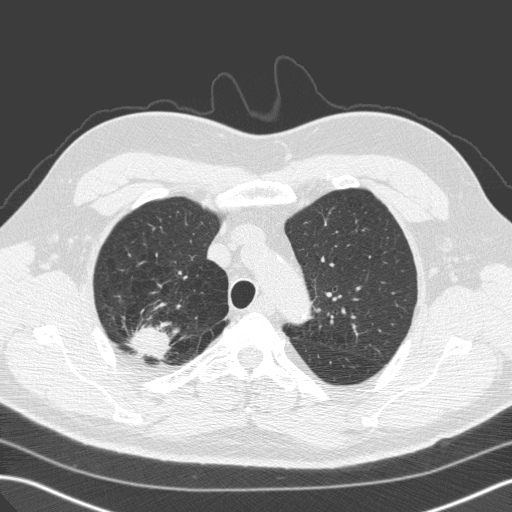
Axial slice from a low-dose chest CT screening exam. Baseline annual screen. Lung window (W 1500 / L -600 HU). 2 mm slice thickness. Standard (soft-tissue) reconstruction kernel (C). Slice 28 of 149 in the series. Male, age 59 years at enrolment.
Expert reader's lesion annotation, bounding box [x1, y1, x2, y2] px = [118, 312, 180, 367]. Screening reader's record for this exam (one nodule recorded; not confirmed to be the boxed lesion): non-calcified nodule or mass ≥4 mm, right upper lobe, 28 × 25 mm, spiculated (stellate) margins, soft tissue attenuation. Official screen result: positive, change unspecified: nodule(s) >= 4 mm or enlarging nodule(s), mass(es), or other non-specific abnormalities suspicious for lung cancer. Participant outcome: lung cancer diagnosed 64 days after this screen — large cell carcinoma, NOS, right upper lobe, undifferentiated (G4), stage IA (AJCC 6th edition), 25 mm at pathology.